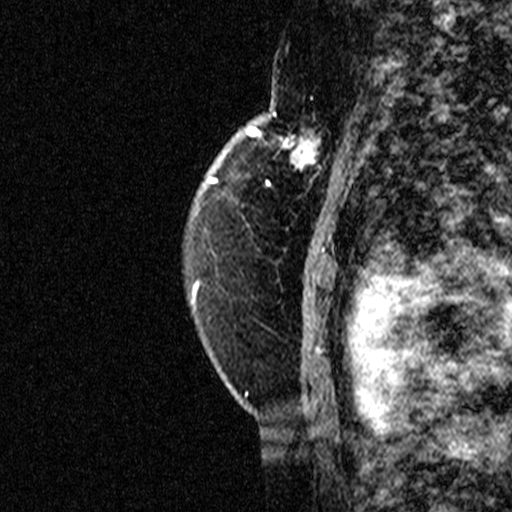
Breast MRI (dynamic contrast-enhanced), one sagittal slice; slice 31 of 44 in the series (ordered by position); dynamic contrast-enhanced study with each time point stored as its own series, time point 2 of 3 at this slice position (early post-contrast, ordered by acquisition time); 1.5 T; TE 4.5 ms, TR 11 ms; 512 × 512 image matrix, field of view 200 × 200 mm. Female patient, age 49 years. From the clinical record (not read from this slice): setting: breast cancer imaged before/during neoadjuvant chemotherapy; receptor status: triple-negative.
Structures marked on this image (semi-automatically segmented with operator editing):
- analysis volume of interest (the breast-tissue region the enhancement analysis was run in; not a lesion): bounding box [x1, y1, x2, y2] px = [254, 112, 347, 207]
- tumour enhancement mask (voxels above the 90 % enhancement threshold inside the analysis volume of interest): [254, 114, 347, 205]